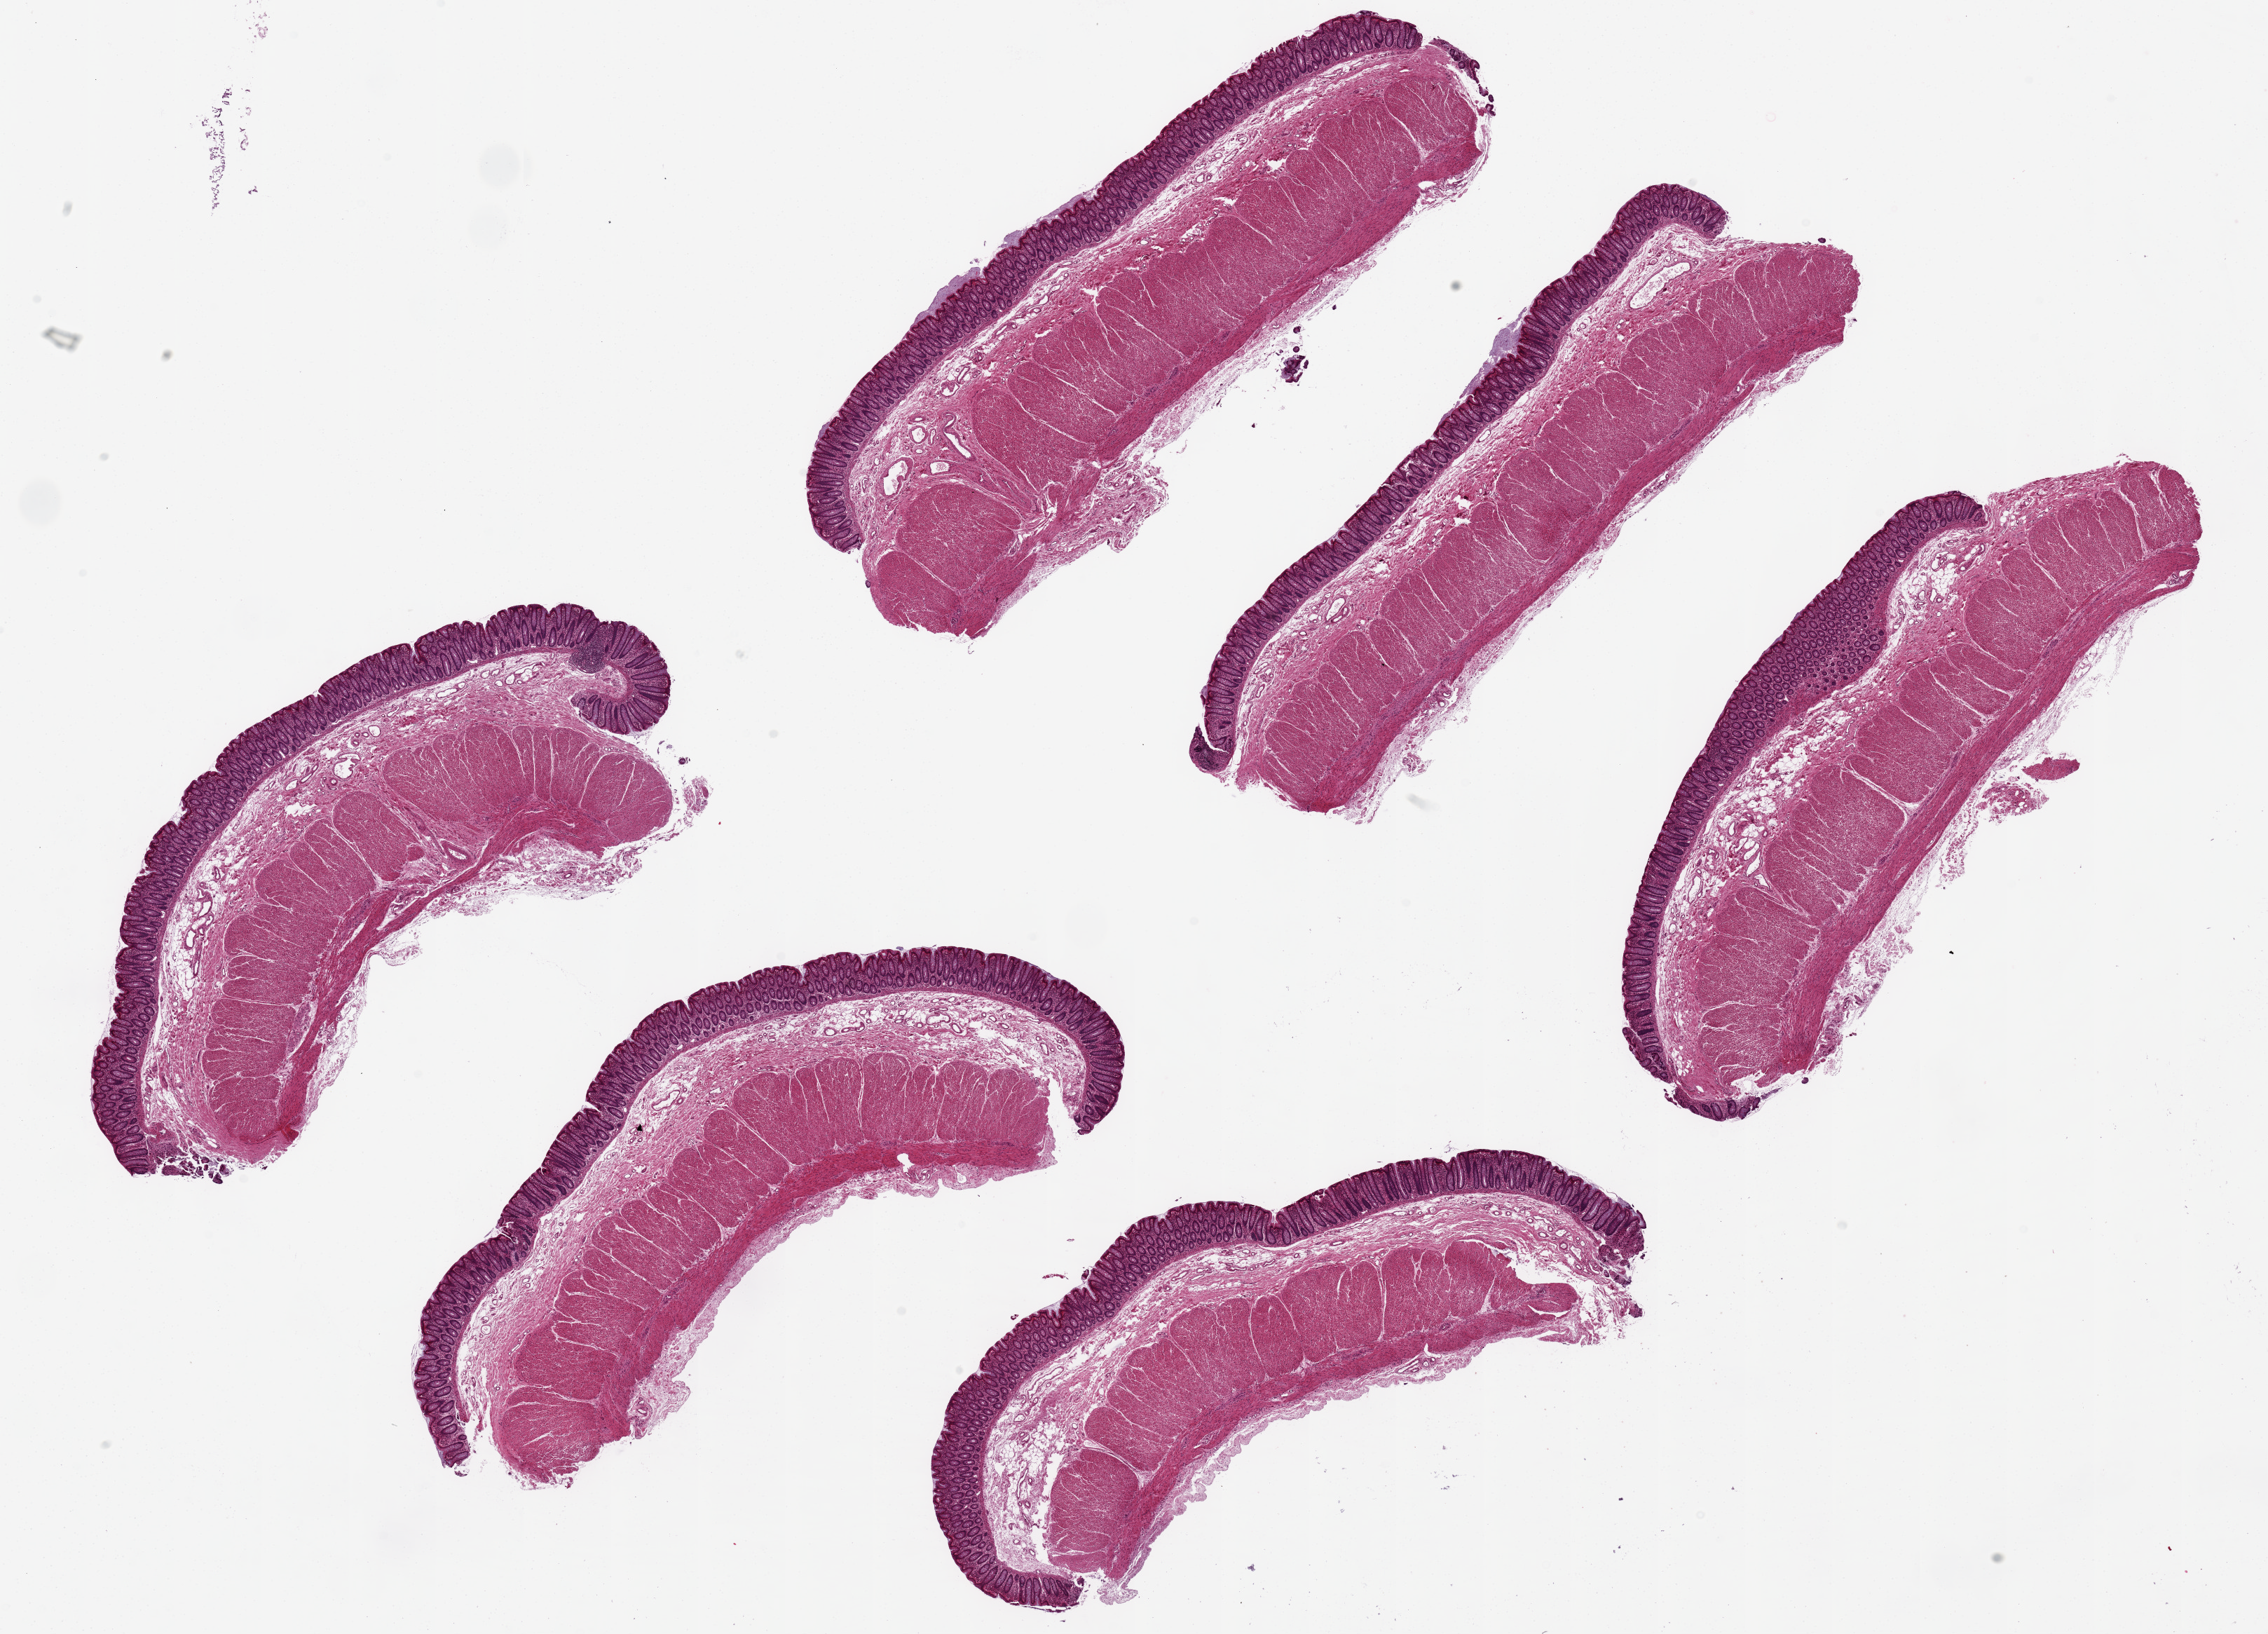
Hematoxylin and eosin (H&E) whole-slide image, brightfield — whole scanned area (about 25.6 x 18.4 mm, from a 20x scan) shown as a low-resolution overview; PAXgene-fixed, paraffin-embedded tissue; section of transverse colon (target tissue); tissue donor sample.
Pathologist's review note for this sample: 6 ~8.5x3m pieces. Mucosa is well-preserved, ~ 15% of thickness.